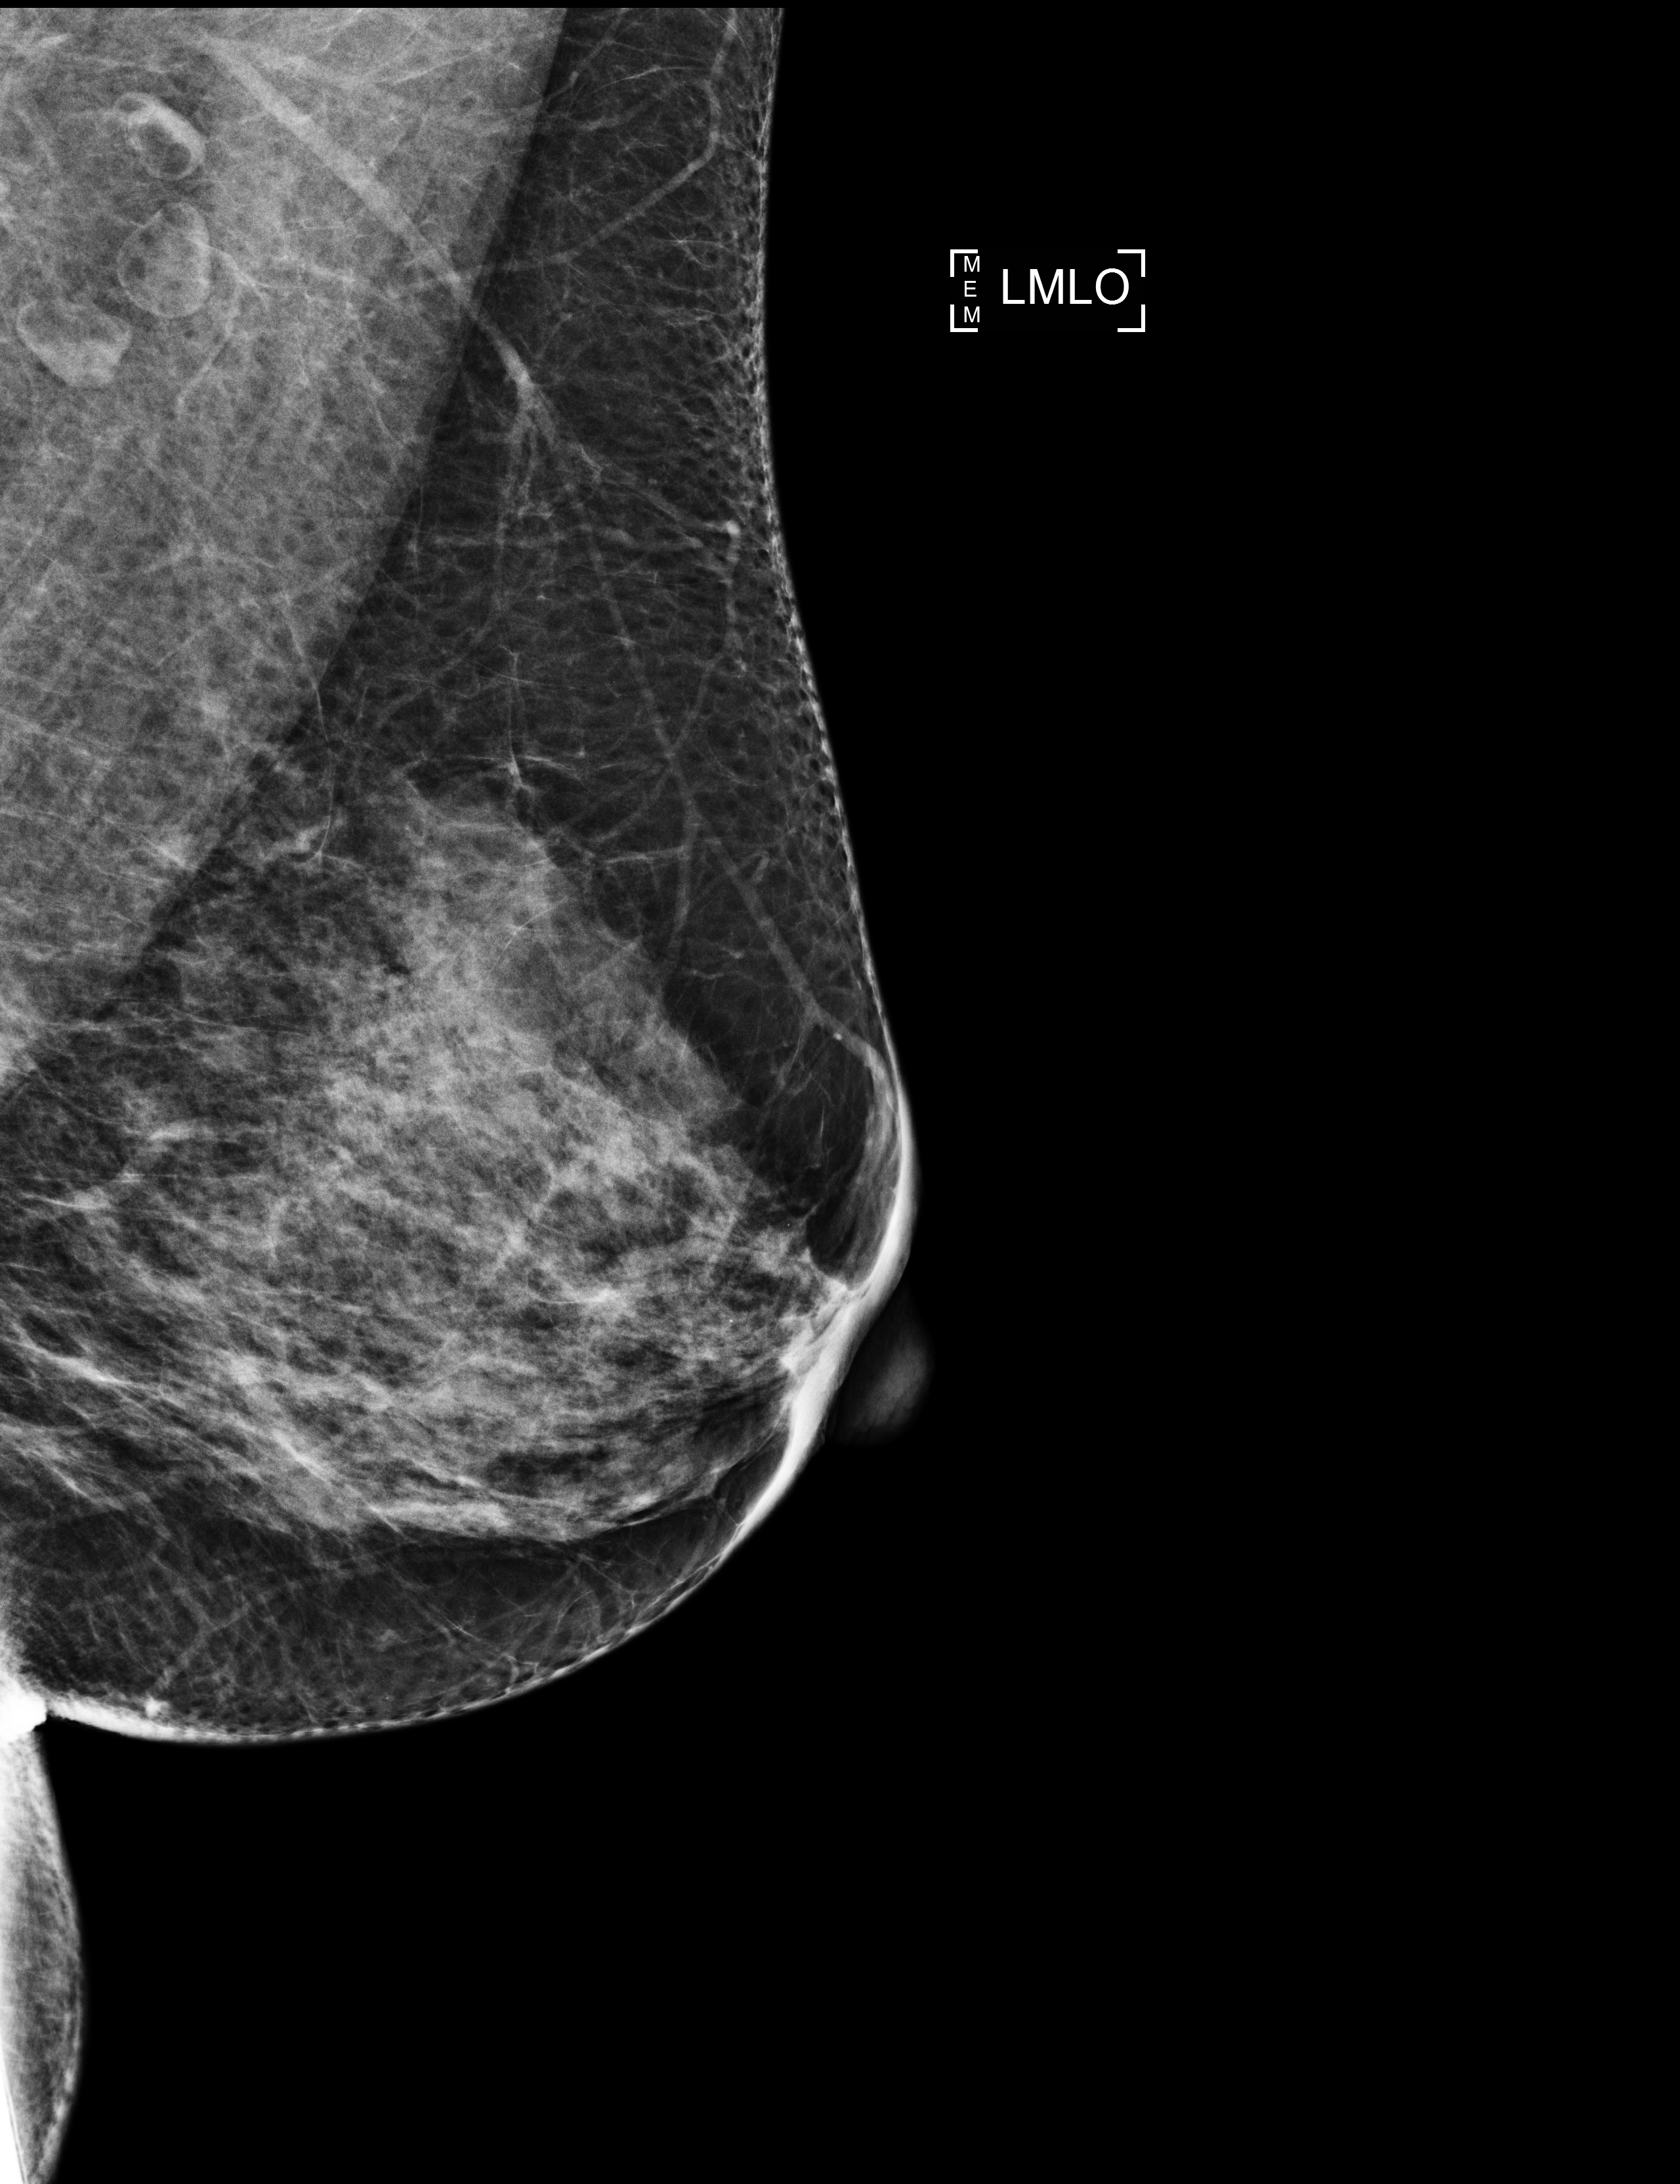
Full-field digital mammogram (FFDM); left breast; mediolateral oblique (MLO) view; screening examination. Female patient, age 57 years.
- breast density at the screening exam (both breasts): heterogeneously dense (BI-RADS density category c)
- final BI-RADS assessment for this screening round (tomosynthesis exam, both breasts): category 1
- recall: no recall after this screen